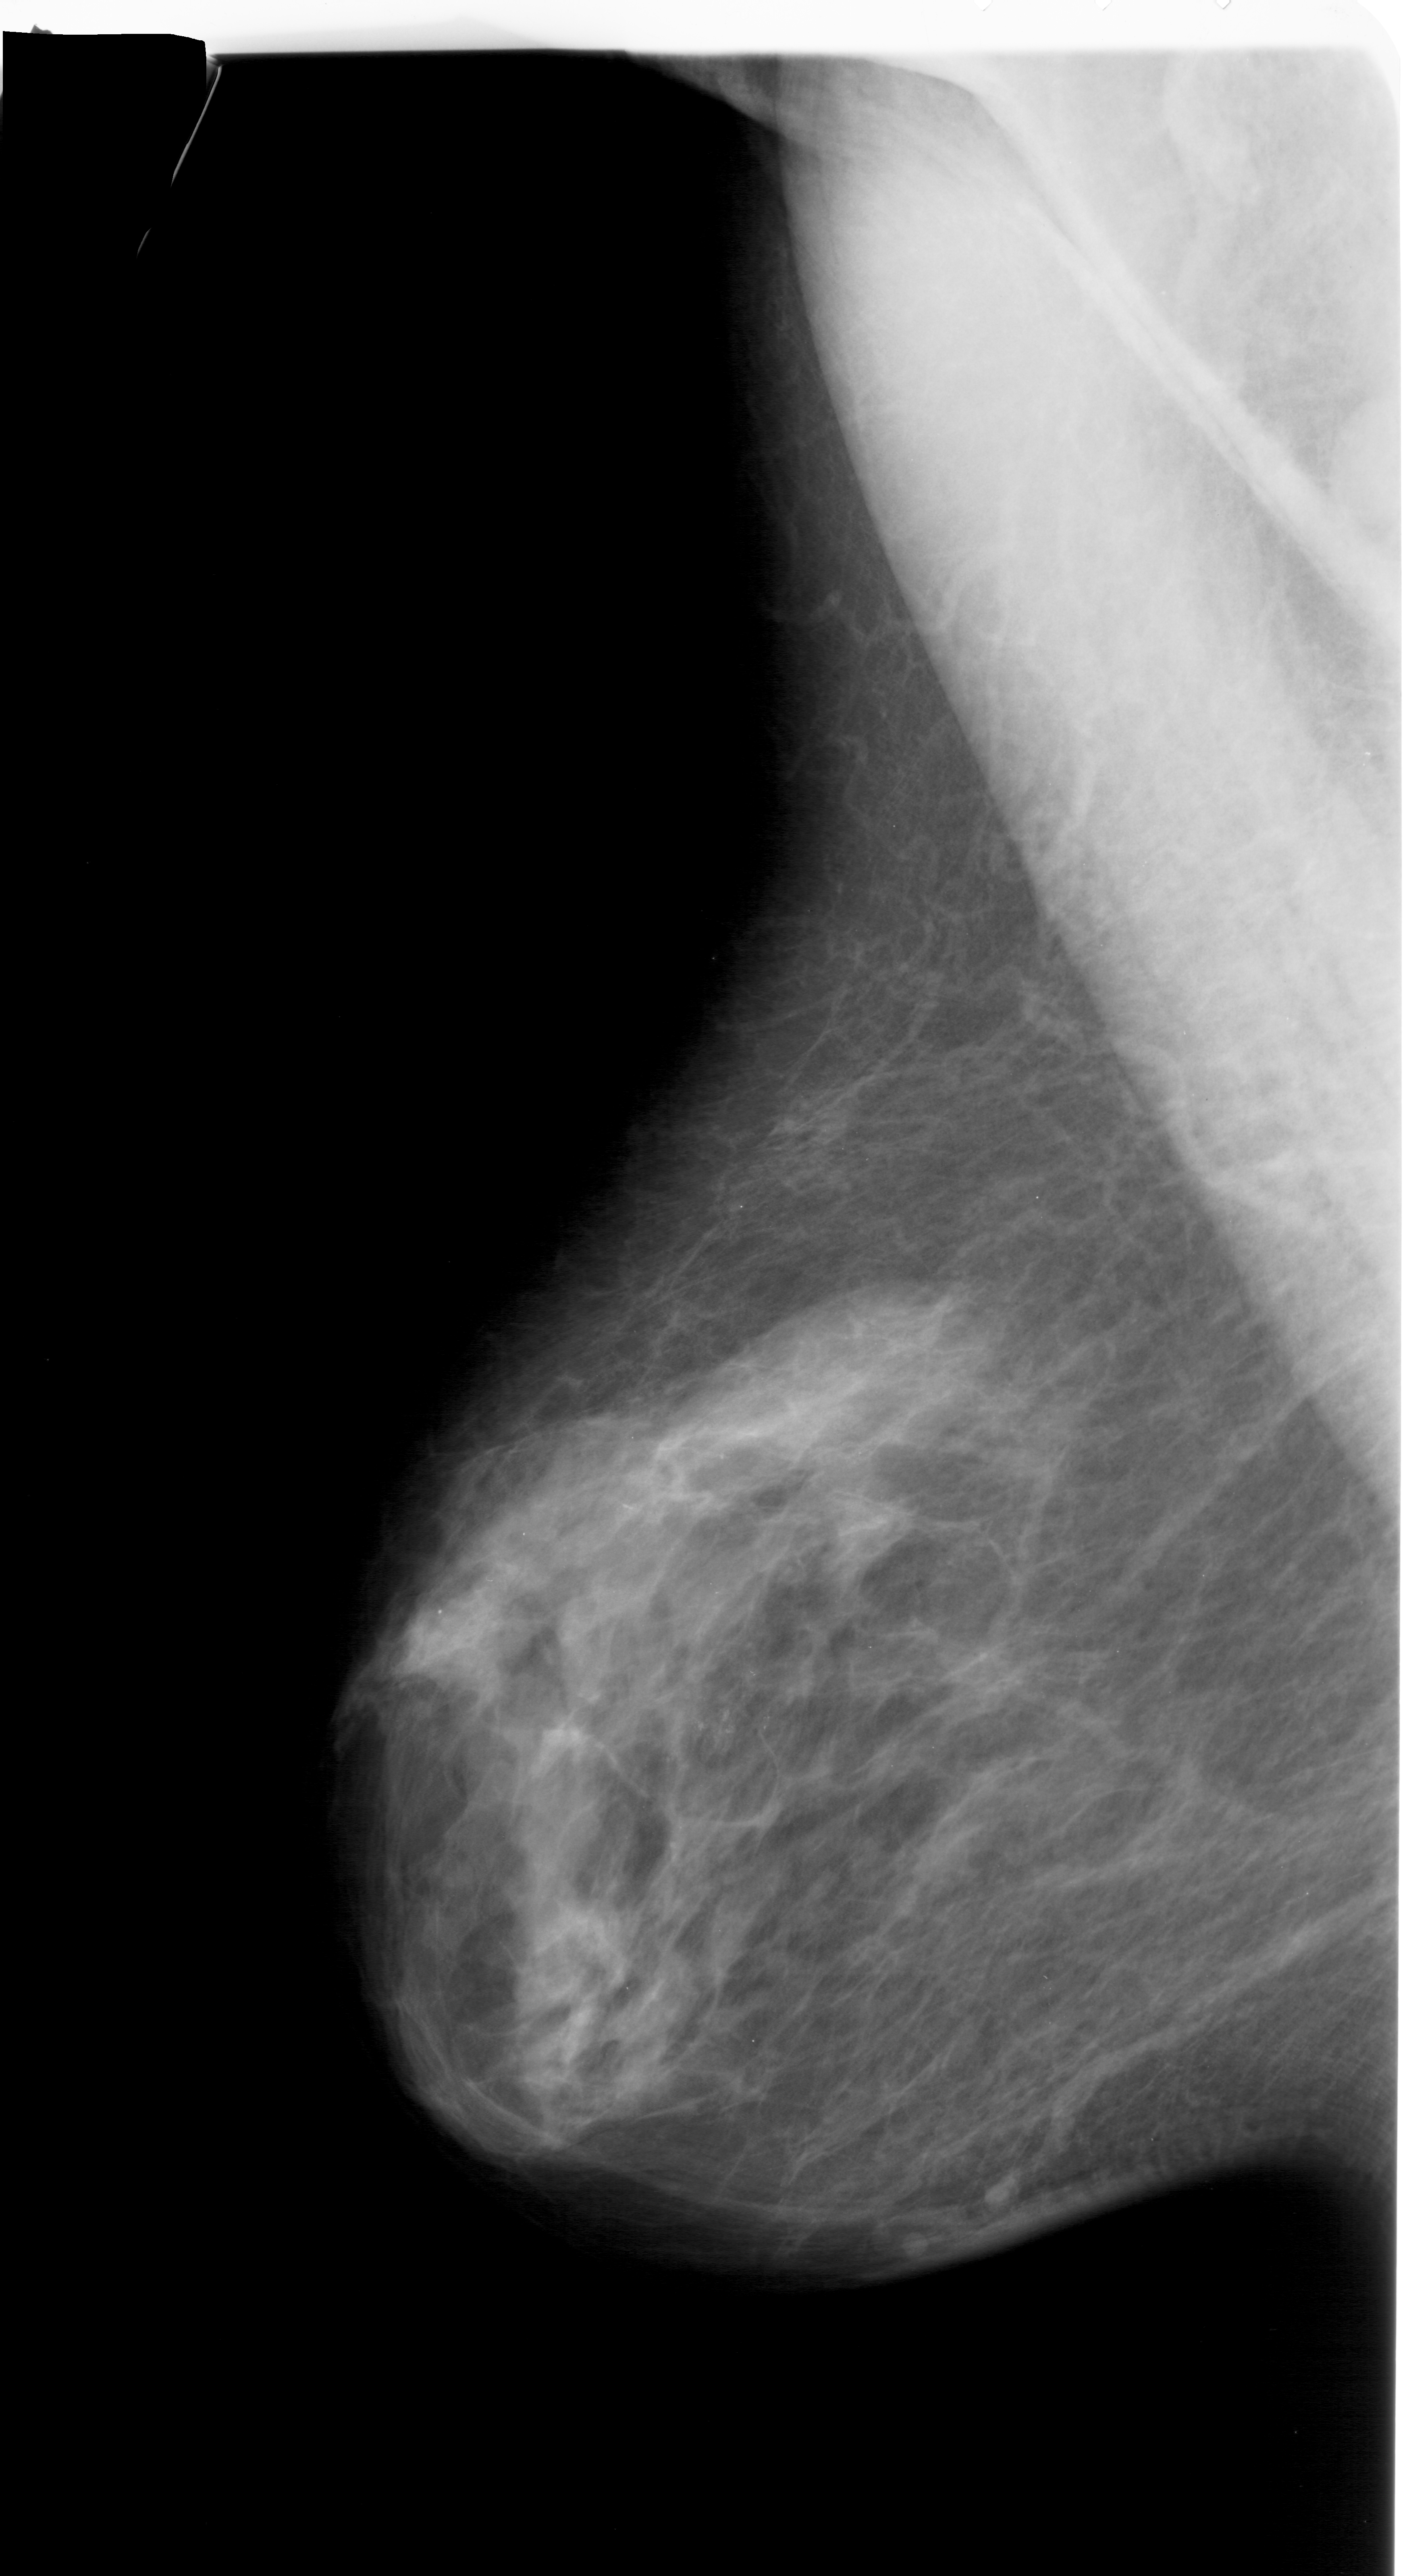
Mammogram (digitized film); left breast; MLO view; BI-RADS breast density category 3 (scale 1–4).
- Marked findings (only marked abnormalities are described; nothing is implied about the rest of the image): calcifications, morphology pleomorphic, distribution clustered; BI-RADS assessment category 4; subtlety rating 3 on a 1 (subtle) to 5 (obvious) scale; pathology (as recorded): benign.